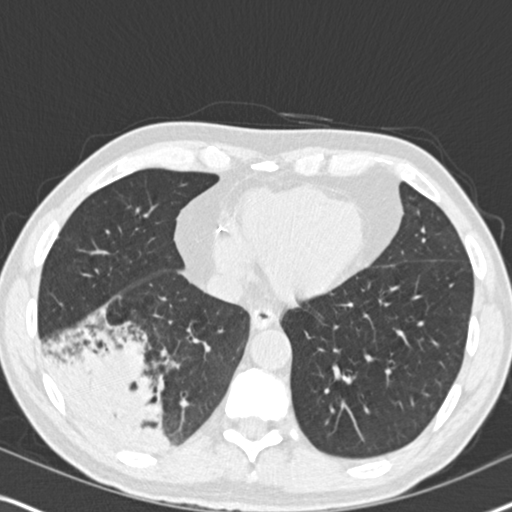
Low-dose screening chest CT, one axial slice; slice 66 of 182 in the series (ordered by position); reconstruction kernel B30f; 120 kVp; lung window (W 1500 / L -600 HU); 2 mm slice thickness; 512 × 512 image matrix, field of view 330 × 330 mm.
Outlined on this slice (expert manual segmentation):
- lesion 1 (tumor, lower lobe of right lung): bounding box [x1, y1, x2, y2] px = [53, 339, 167, 452]